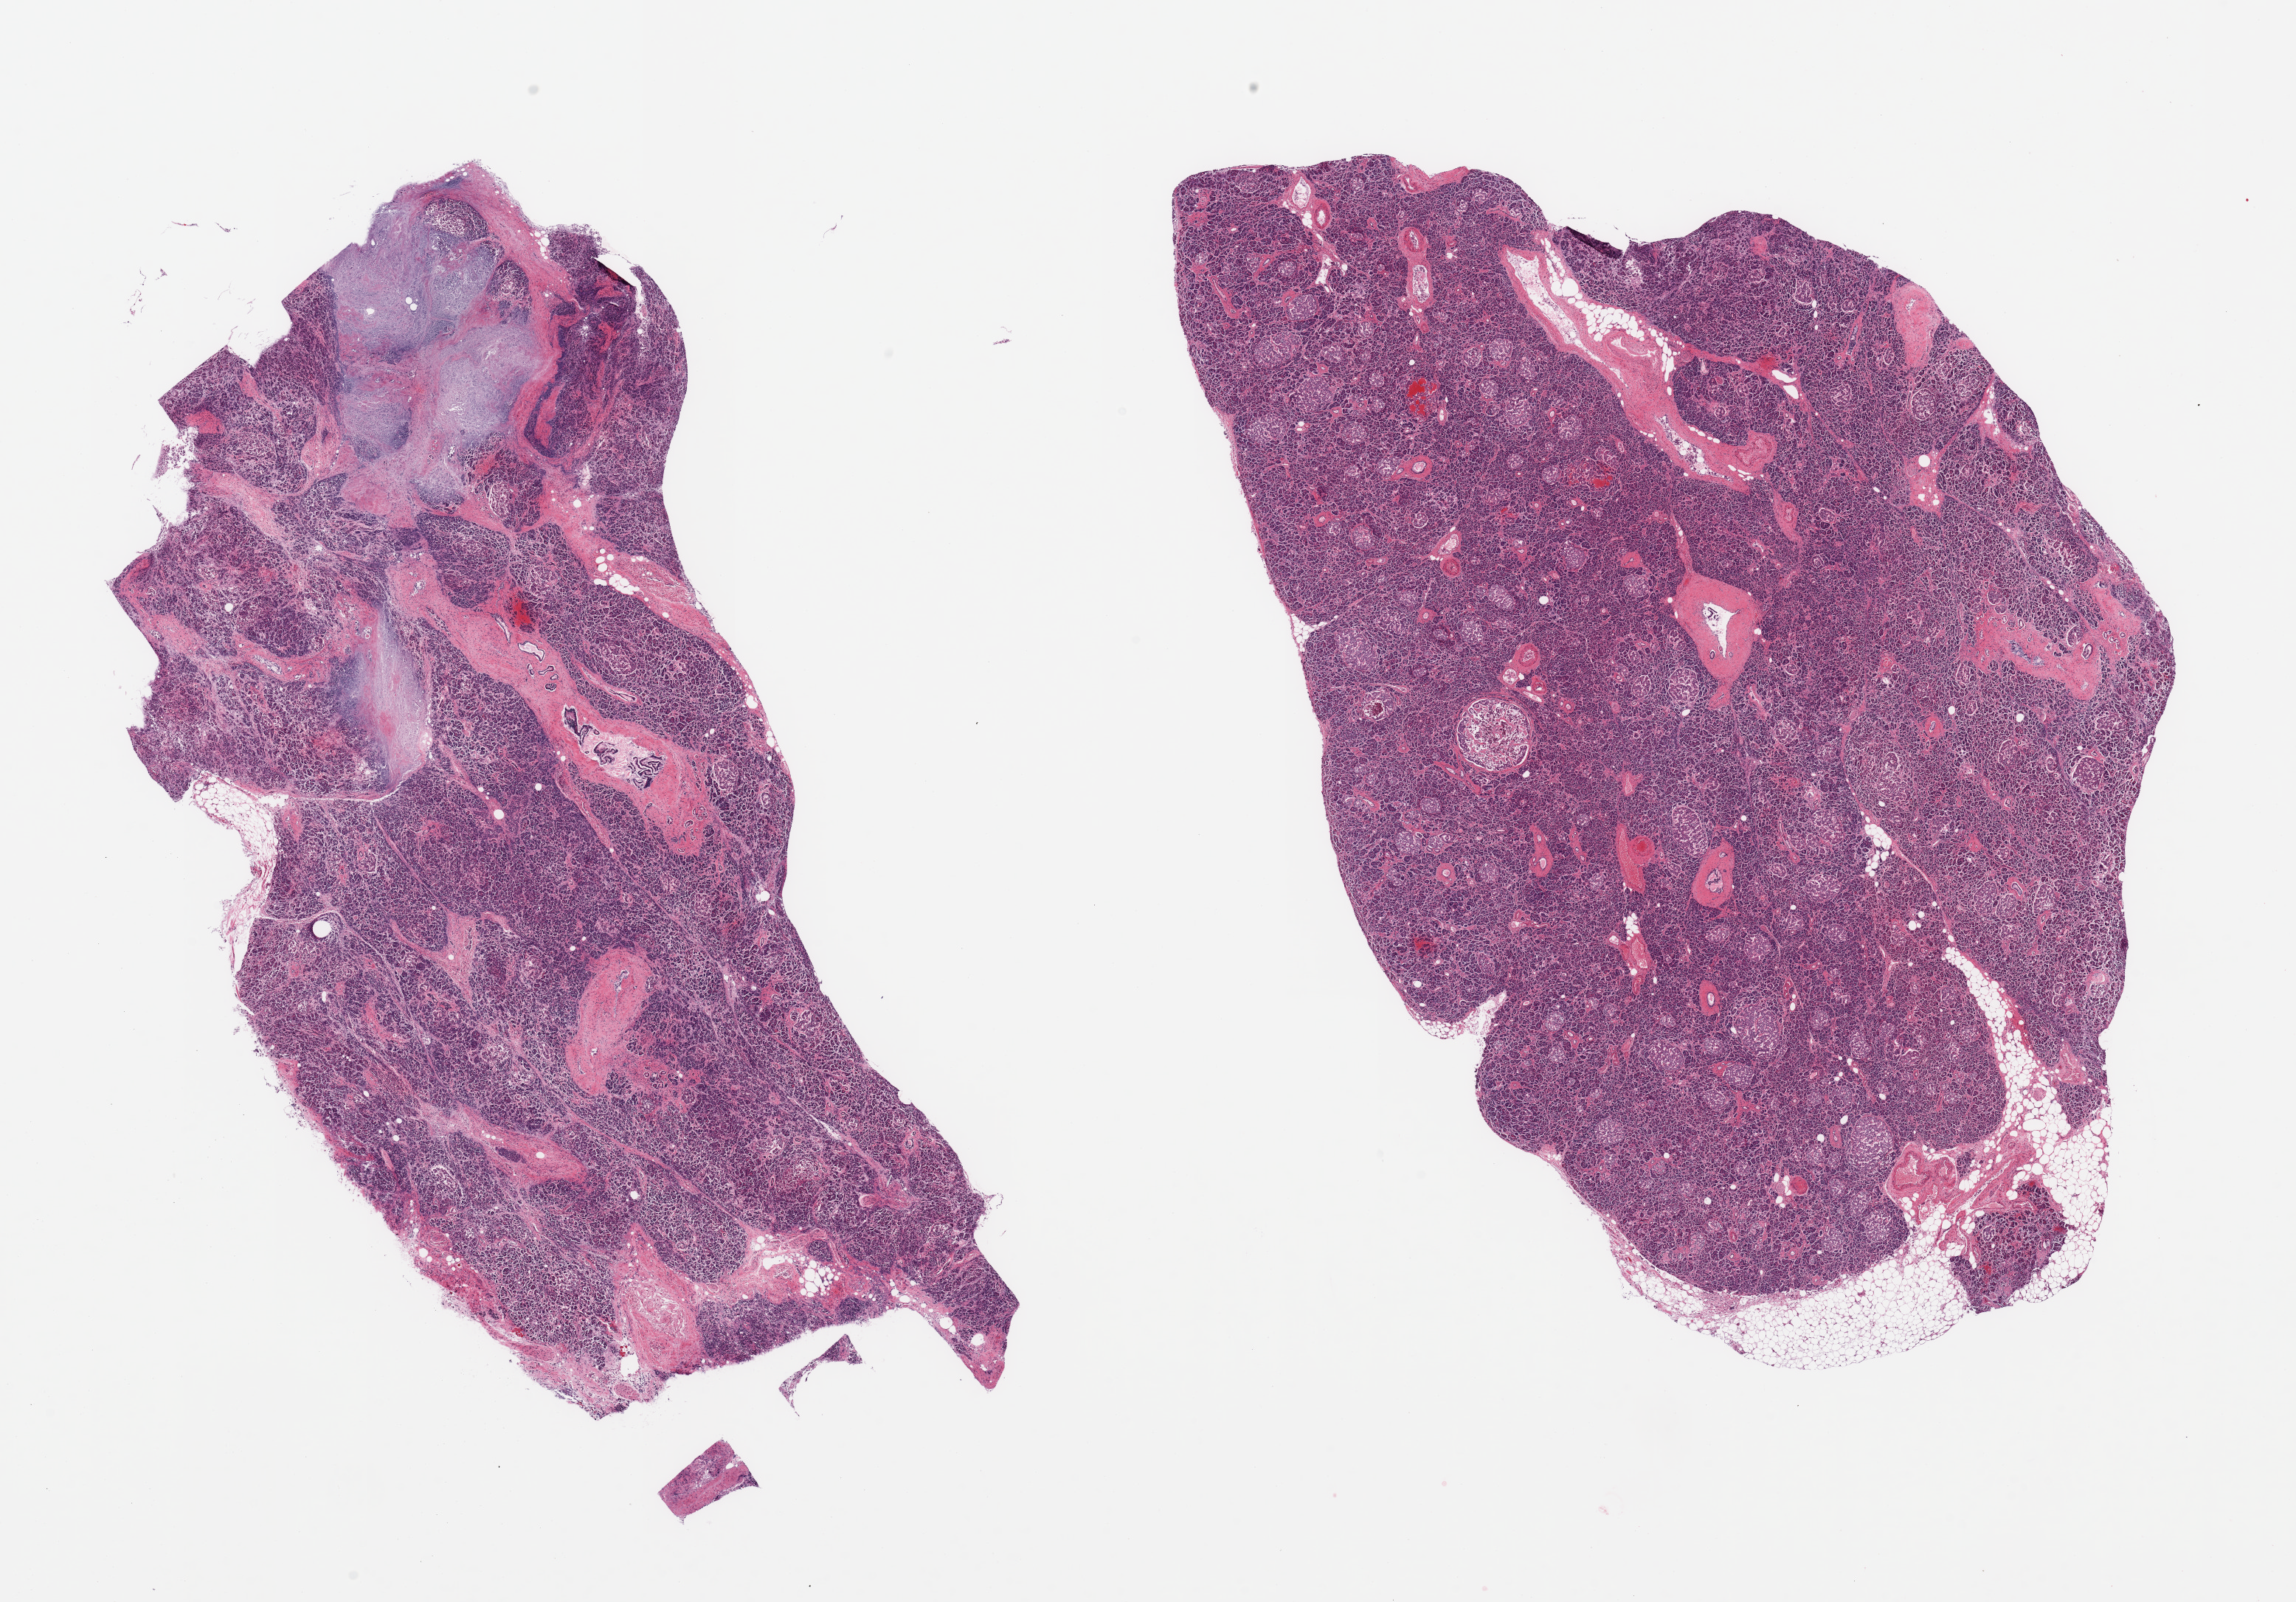
Digitized haematoxylin and eosin-stained section, a low-resolution overview of the entire scanned area, about 24.6 x 17.2 mm (acquisition: 20x scan), PAXgene-fixed, paraffin-embedded tissue, section of pancreas (target tissue), tissue donor sample. Donor sex: male.
• reviewer comment on this tissue sample: 2 pieces variably autolytic; one with well preserved islets; other with advanced saponification -sample carefully